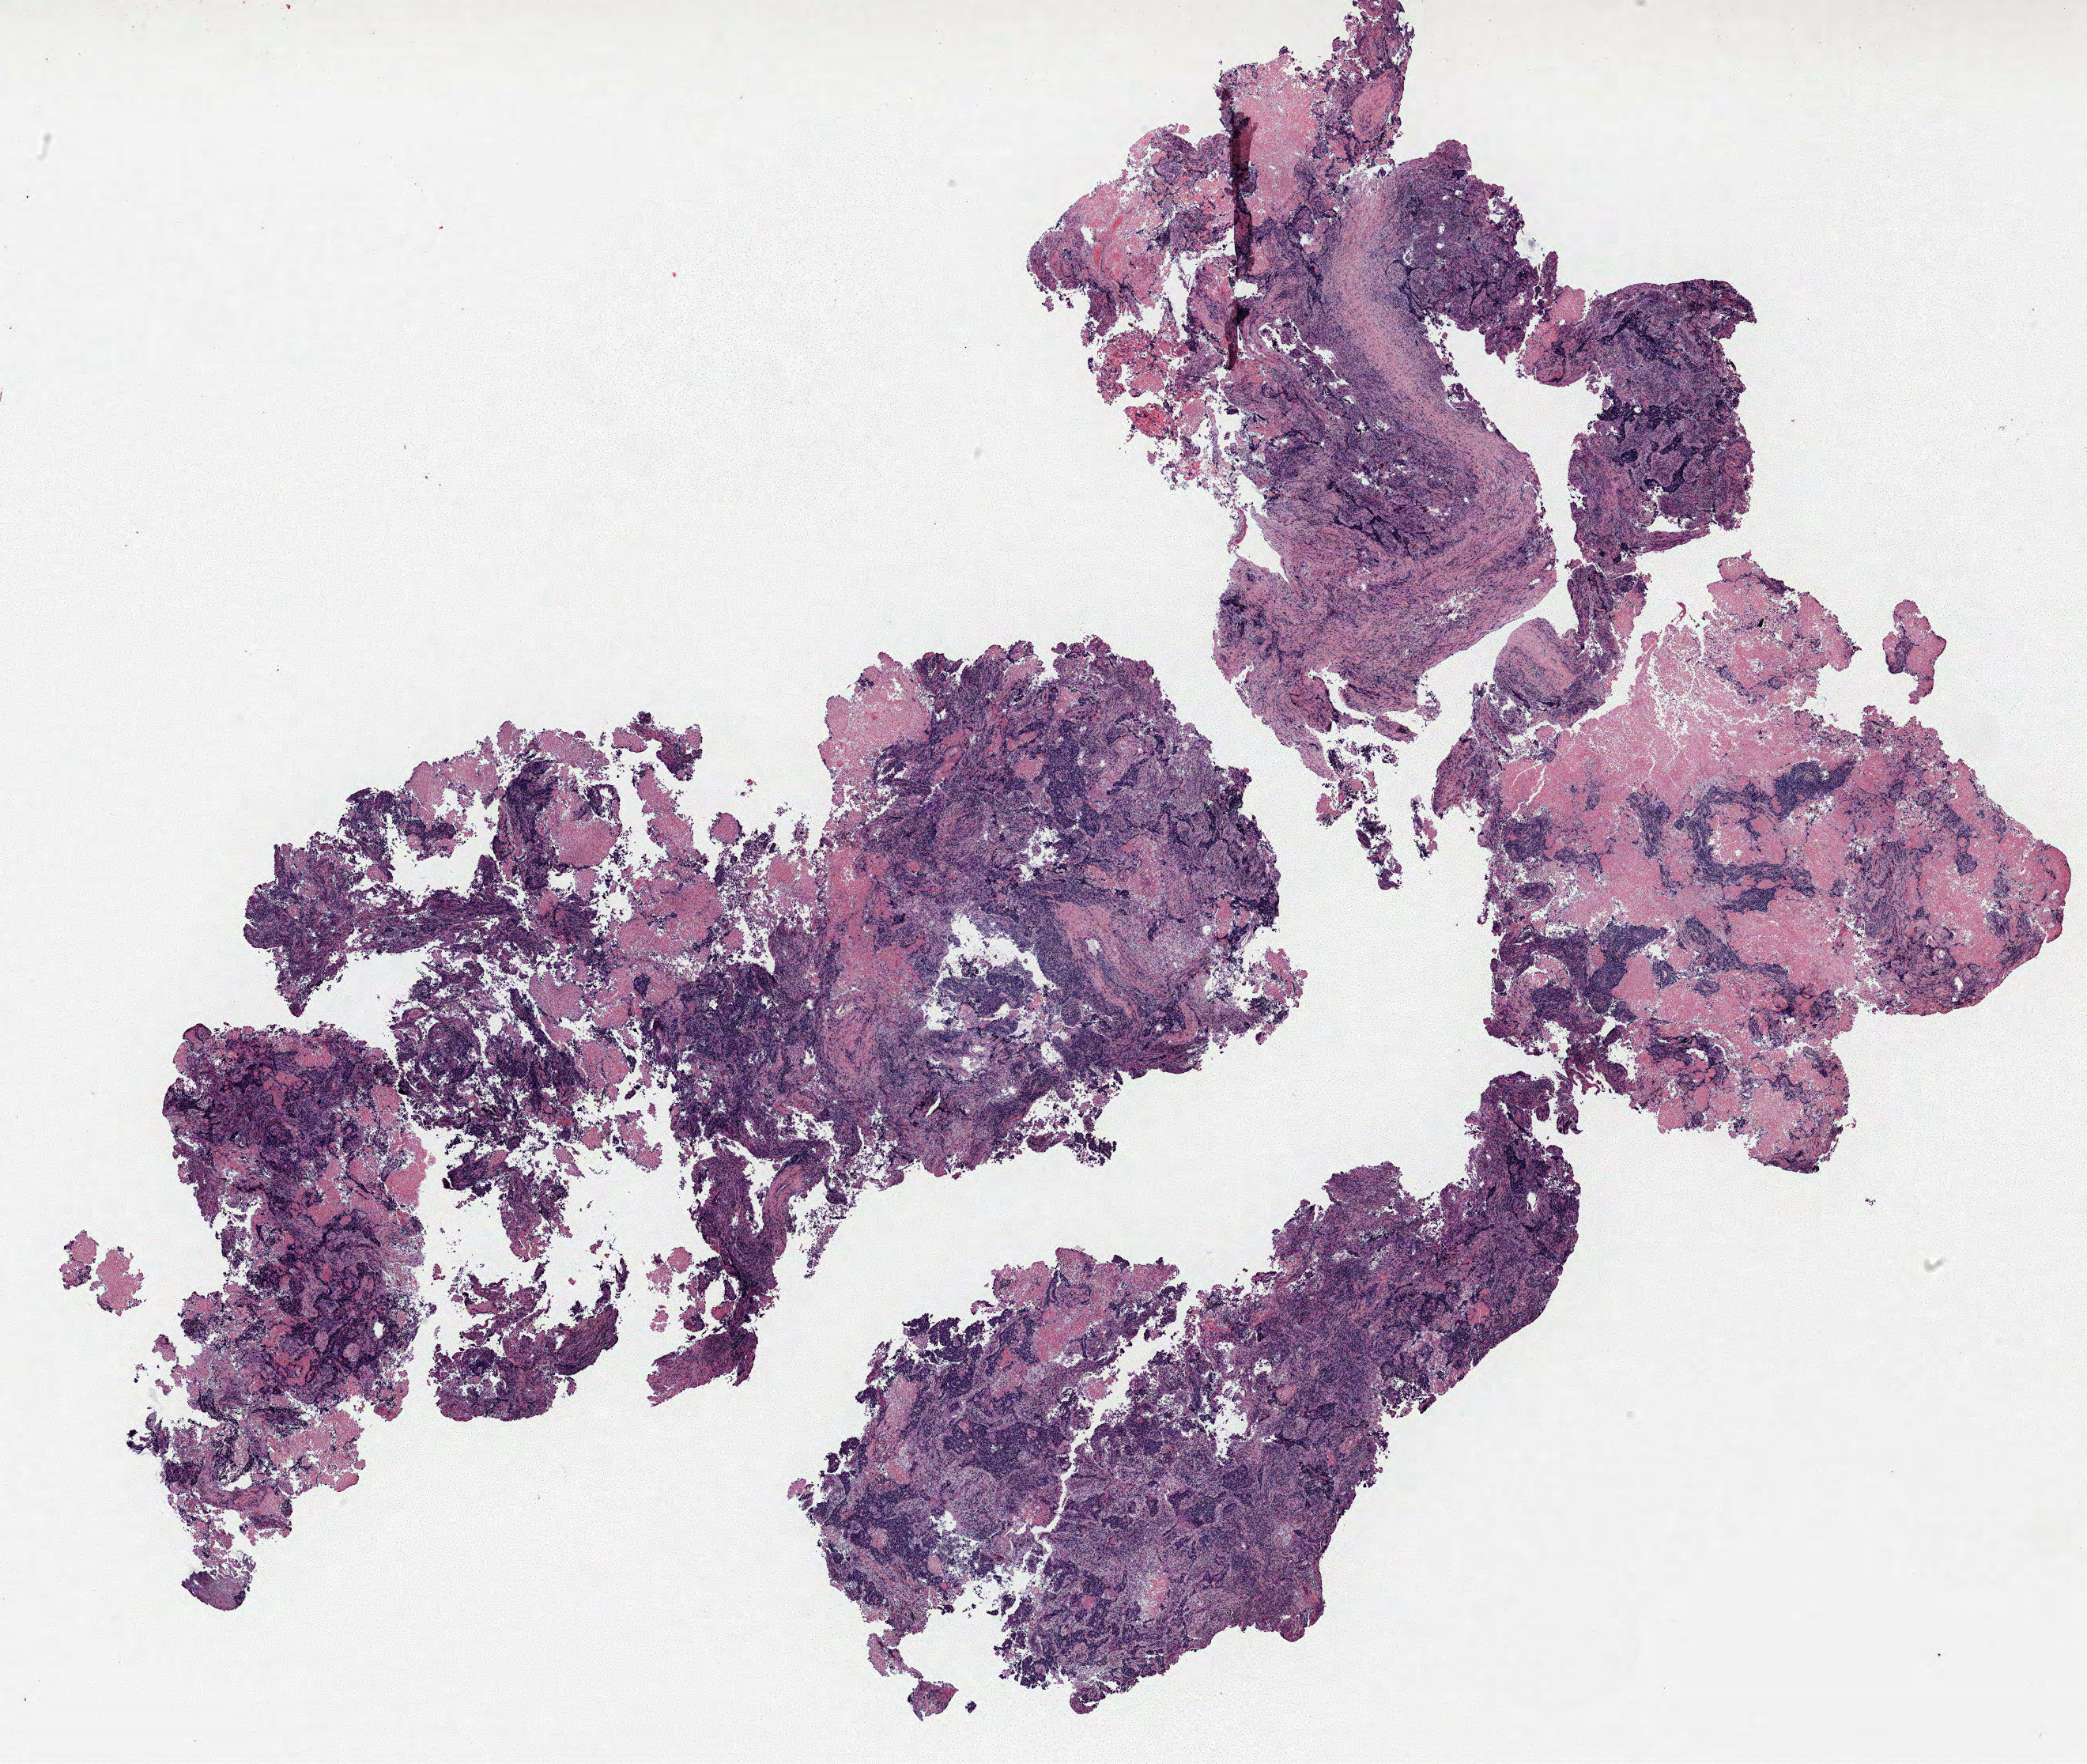
Whole-slide histology image, H&E — low-resolution overview of the scanned area, about 21.1 x 17.9 mm (from a 40x scan); FFPE section; lung tissue. Male patient, aged 59 at enrolment. Current smoker at enrolment. Grade: undifferentiated (G4).
• tumour size (pathology): 50 mm
• participant's lung-cancer diagnosis: Large cell carcinoma, NOS (ICD-O-3 8012/3)
• stage (AJCC 6th edition): IIIB
• primary tumour location (clinical record): left hilum, mediastinum